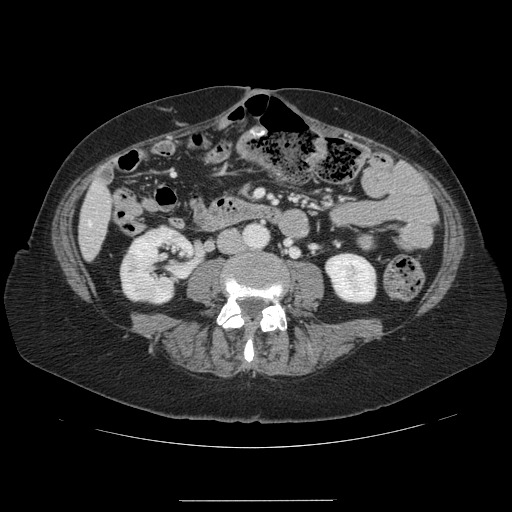
Contrast-enhanced abdominal CT, one axial slice. Slice 19 of 141 in the series (ordered by position). 120 kVp. Intravenous contrast given. Soft-tissue window (W 400 / L 40 HU). 512 × 512 image matrix. Female patient, age 74 years. From the clinical record (not read from this slice): diagnosis: colorectal cancer liver metastases, imaged before liver resection; multiple liver metastases: yes; largest metastasis: 7 cm.
Structures marked on this image (outlined manually by an expert reader):
- hepatic veins: bounding box <88,222,91,225> (left, top, right, bottom; pixels)
- liver: <80,184,112,258>
- planned liver remnant (the part of the liver to remain after resection): <85,199,112,229>